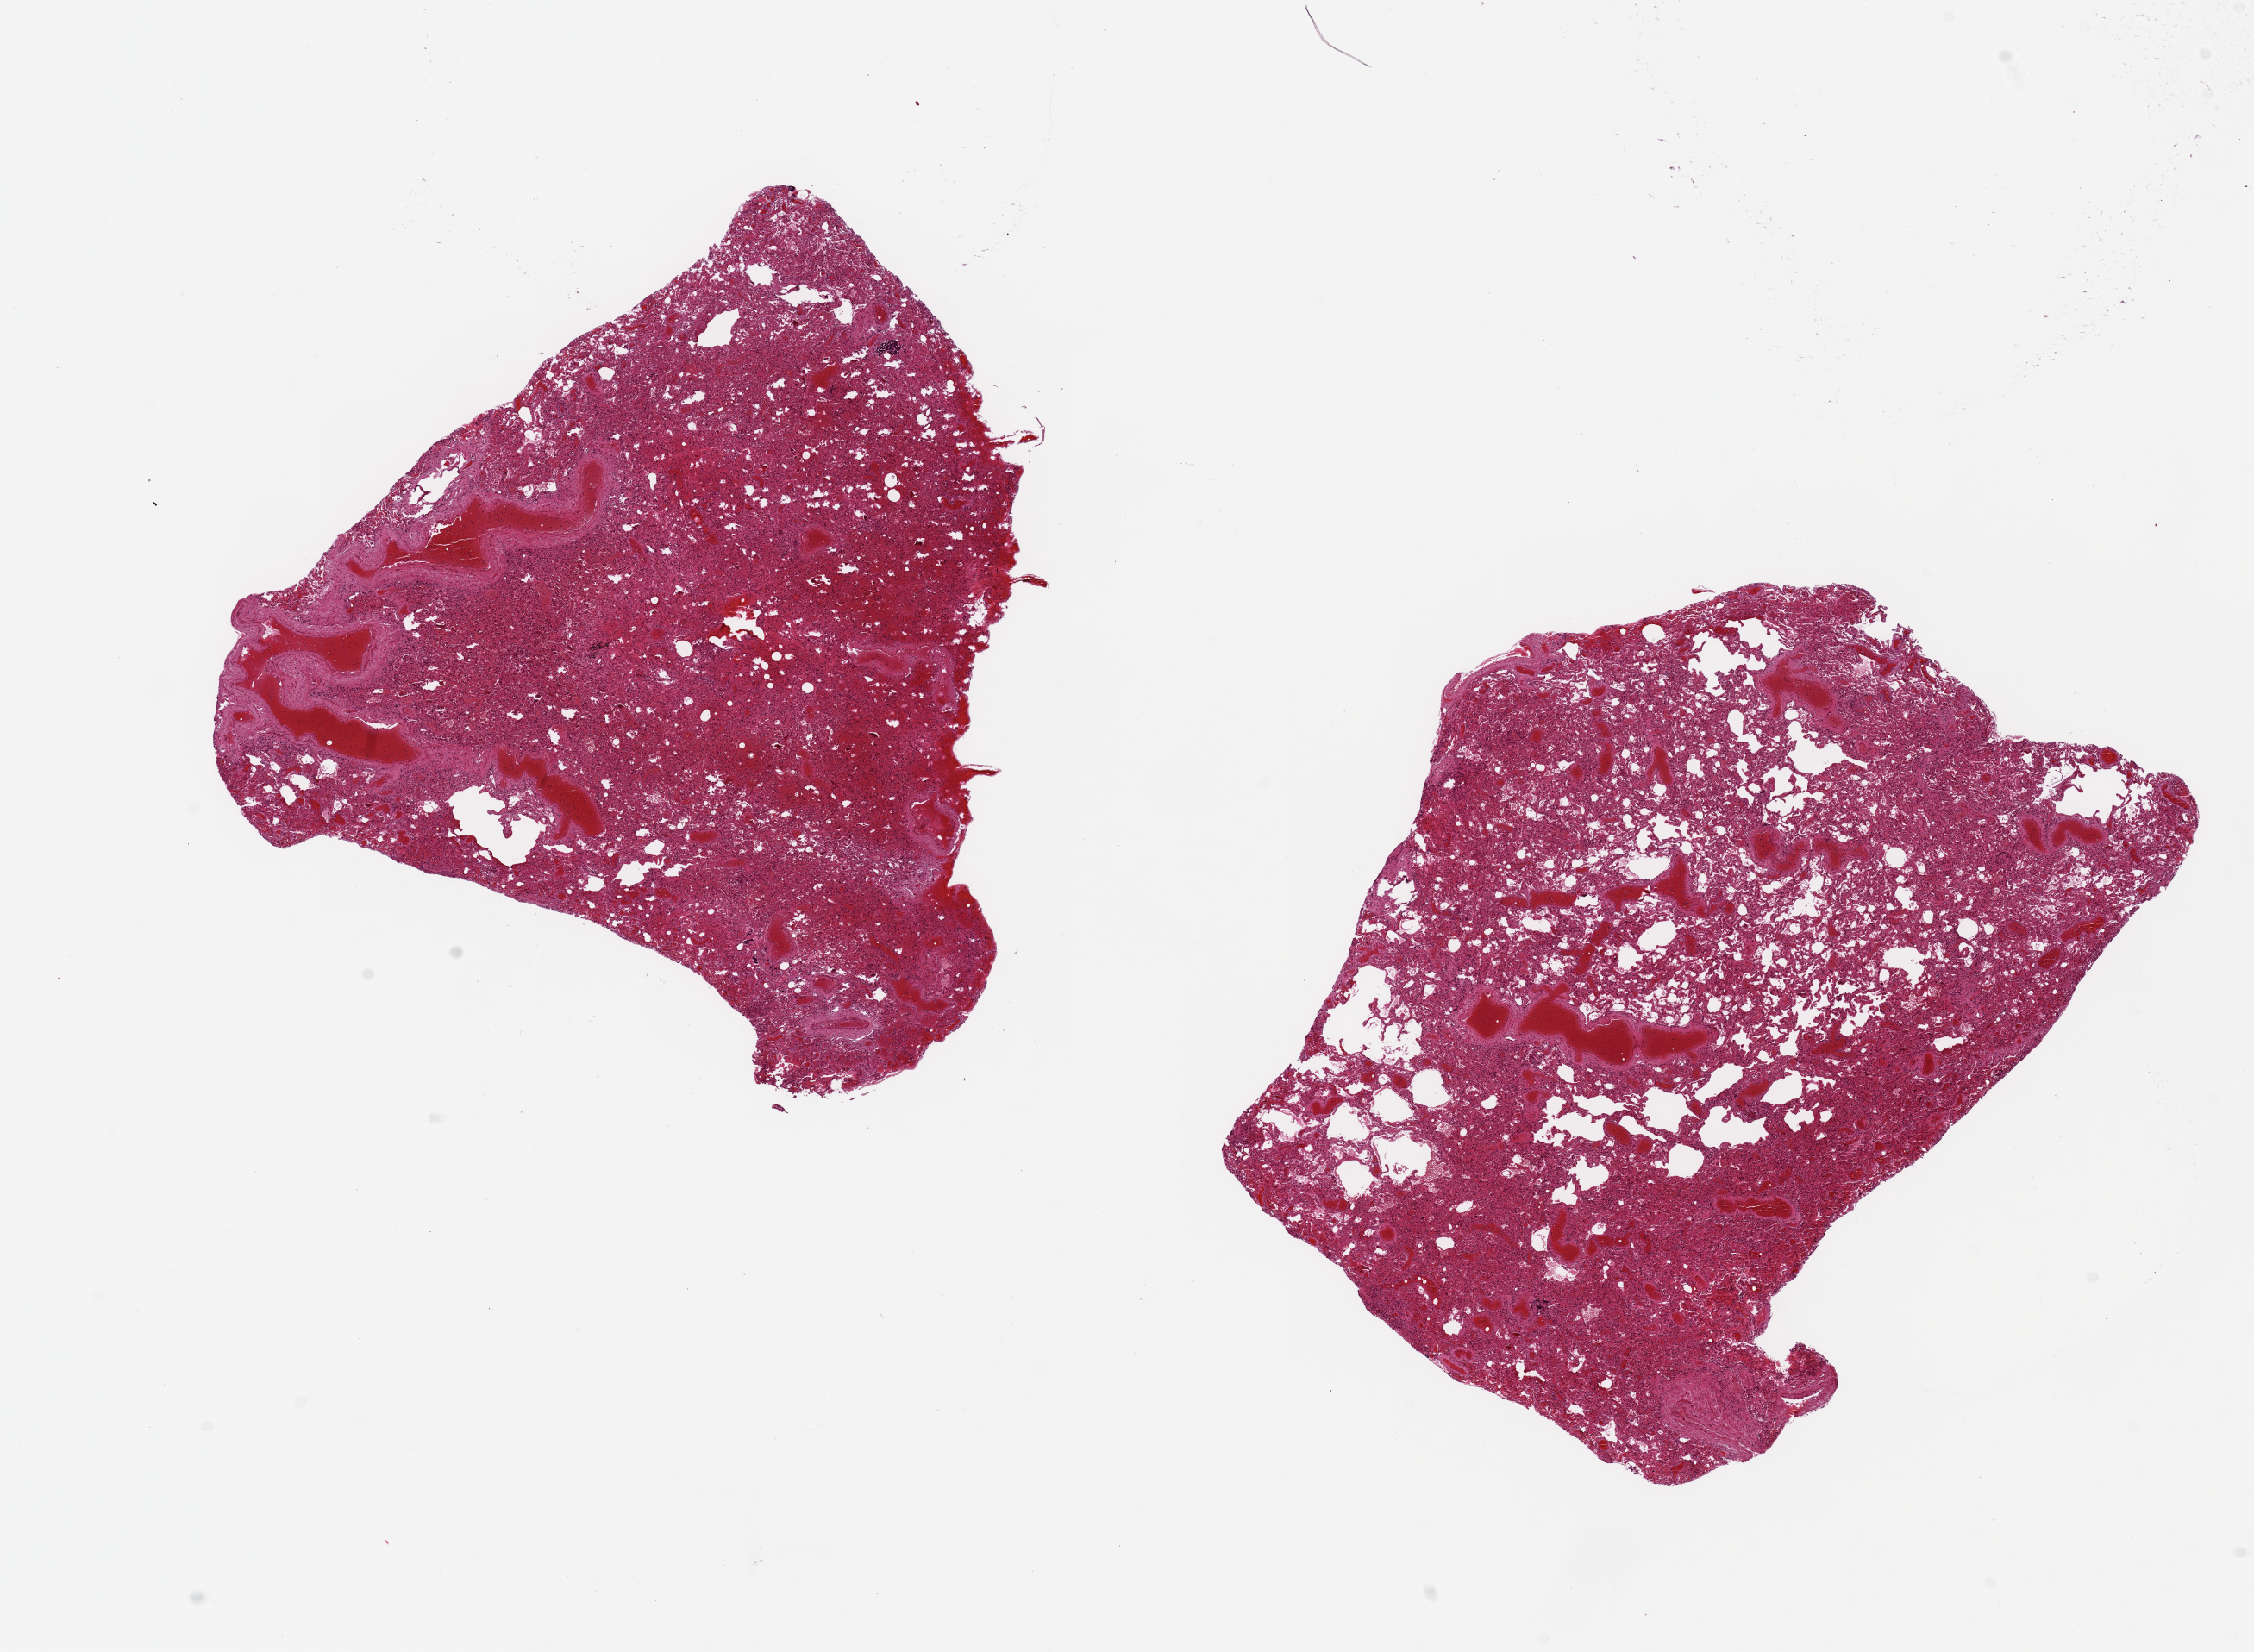
Digitized H&E-stained section, whole scanned area (about 20.7 x 15.2 mm, from a 20x scan) shown as a low-resolution overview. PAXgene-fixed paraffin-embedded (PFPE) section. Sampled site (target tissue): lung. Tissue donor sample. Female donor.
• review note (as recorded): 2 pieces, 7x7 & 8x6mm; markedly congested with focal hemorrhages; minimal air